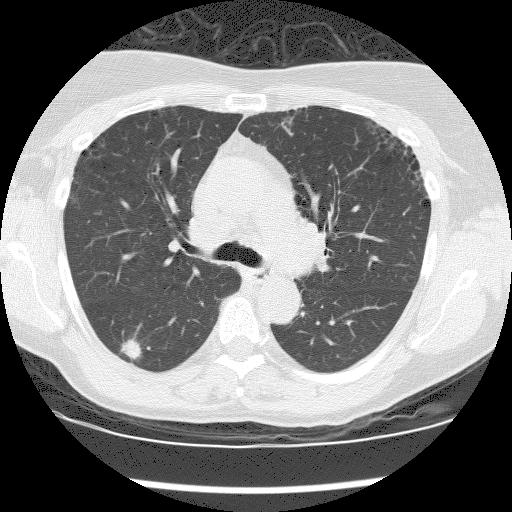
Low-dose screening chest CT, one axial slice; position 120 of 176 along the scan axis; reconstruction kernel BONE; 120 kVp; lung window (W 1500 / L -600 HU); 512 × 512 image matrix.
Outlined on this slice (outlined manually by an expert reader):
- lesion 1 (tumor, lower lobe of right lung): box from (x=120, y=337) to (x=142, y=360) px